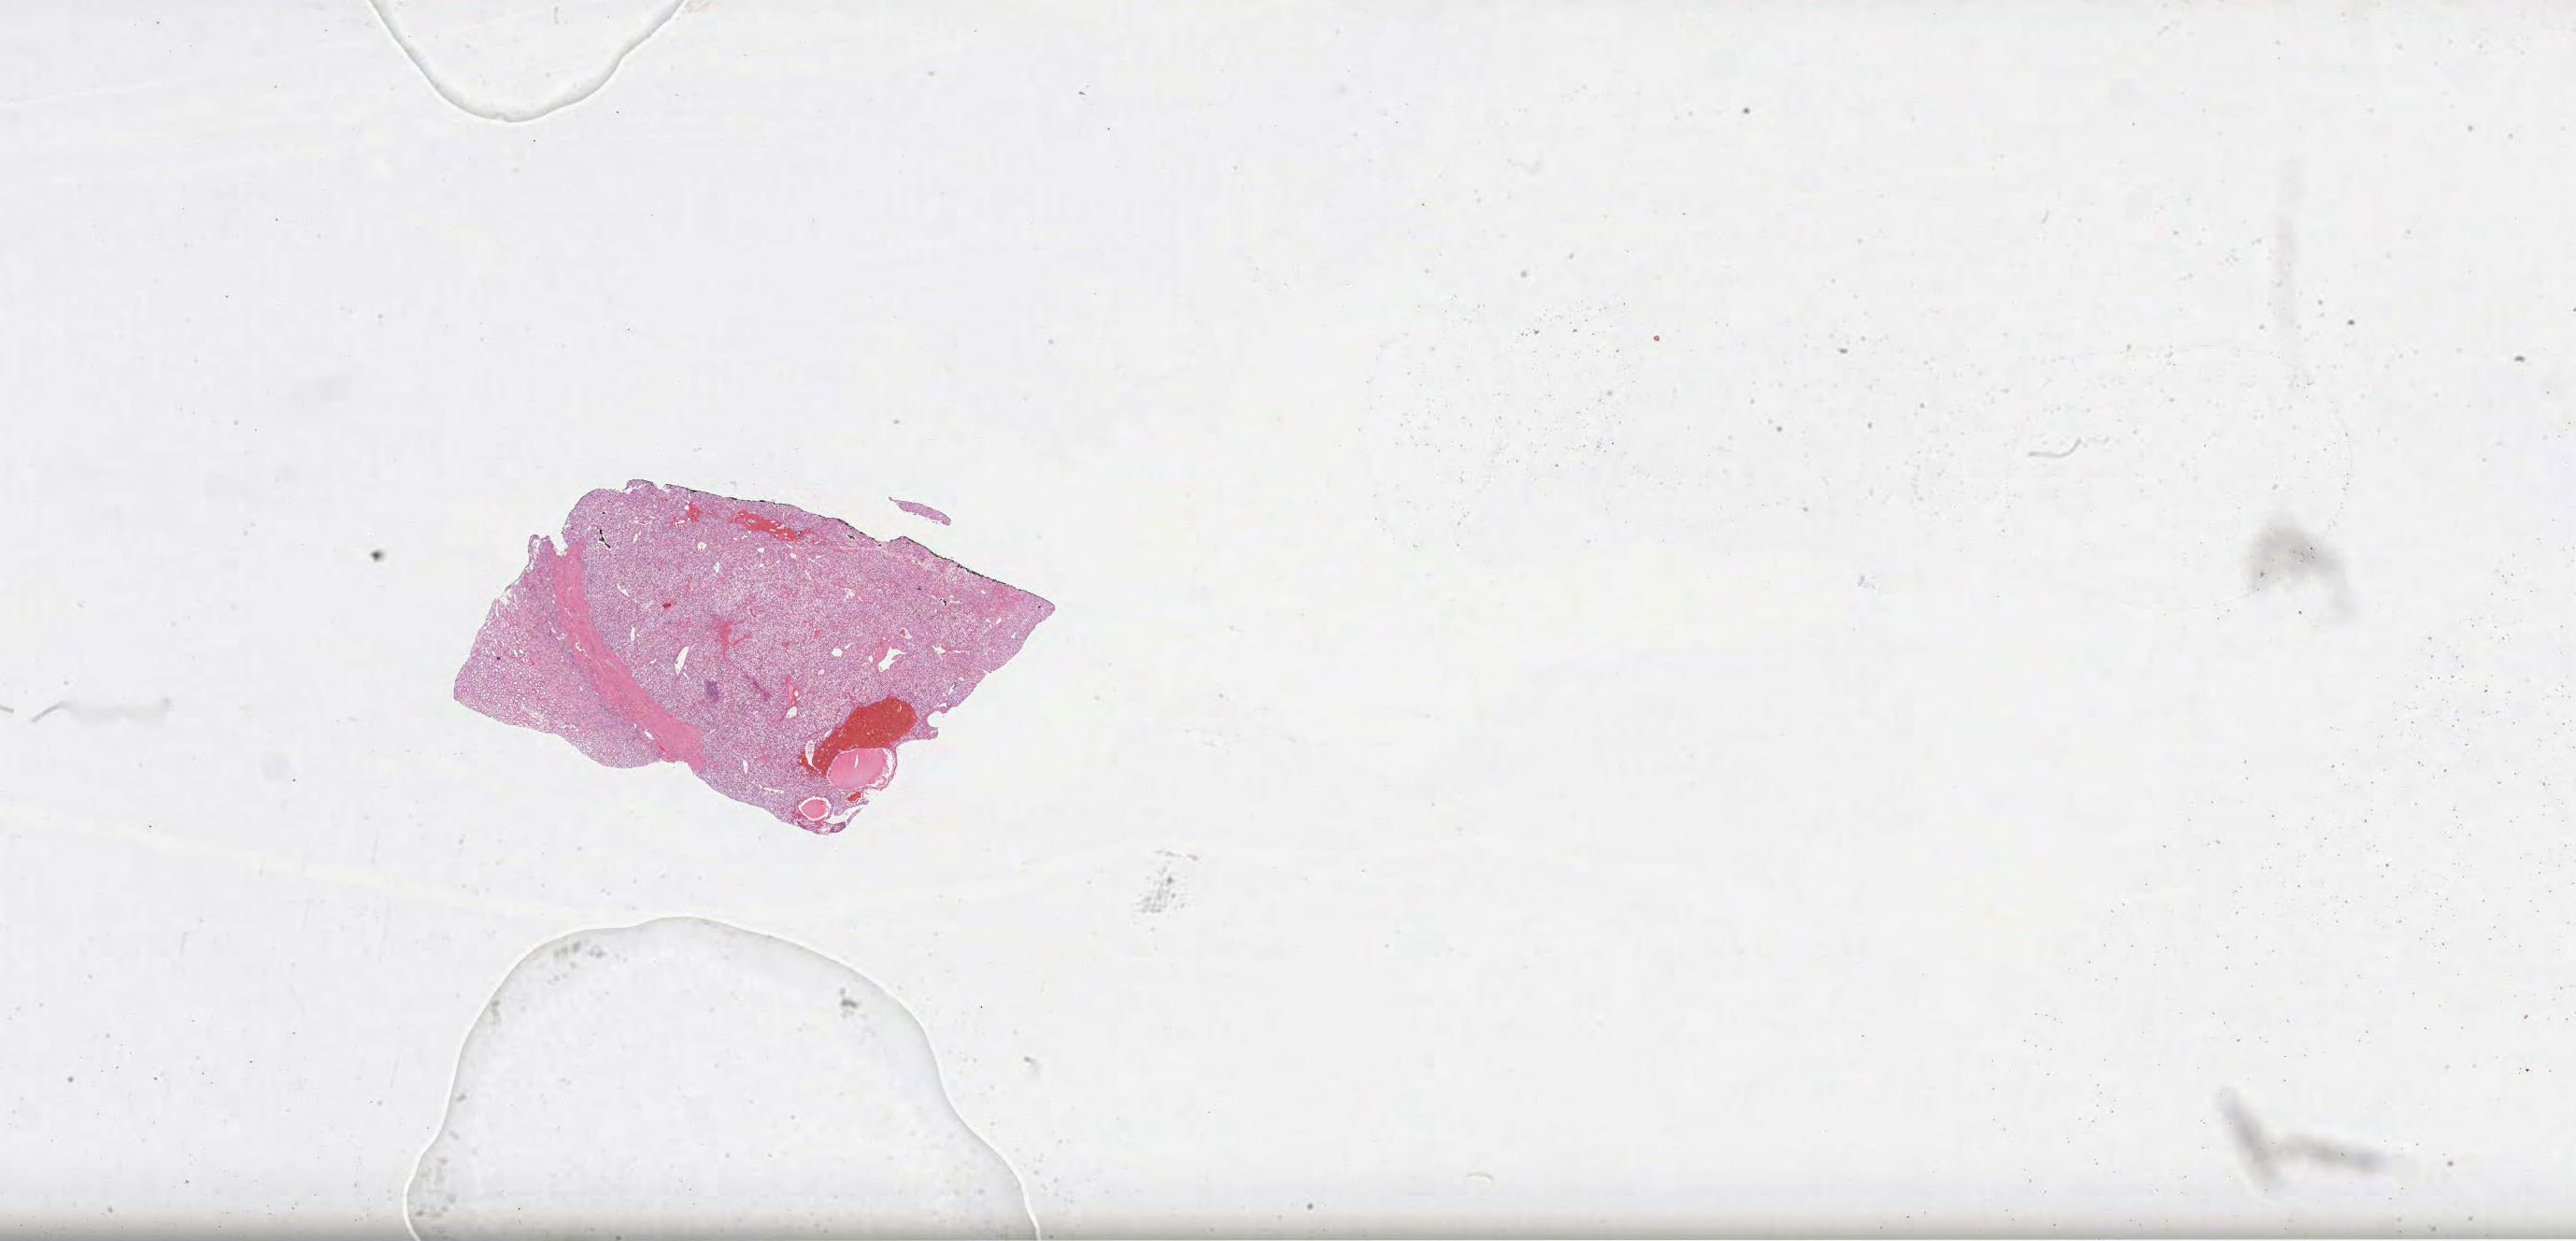
Digitized H&E tissue section (whole slide), low-resolution overview of the scanned area, about 44.5 x 21.4 mm (from a 40x scan). Formalin-fixed paraffin-embedded (FFPE) diagnostic section. Sample: primary tumour, kidney. Male, age 46 years at initial diagnosis. Histologic grade: G2 (moderately differentiated).
Histologic diagnosis: Clear cell adenocarcinoma, NOS. AJCC pathologic stage: I.